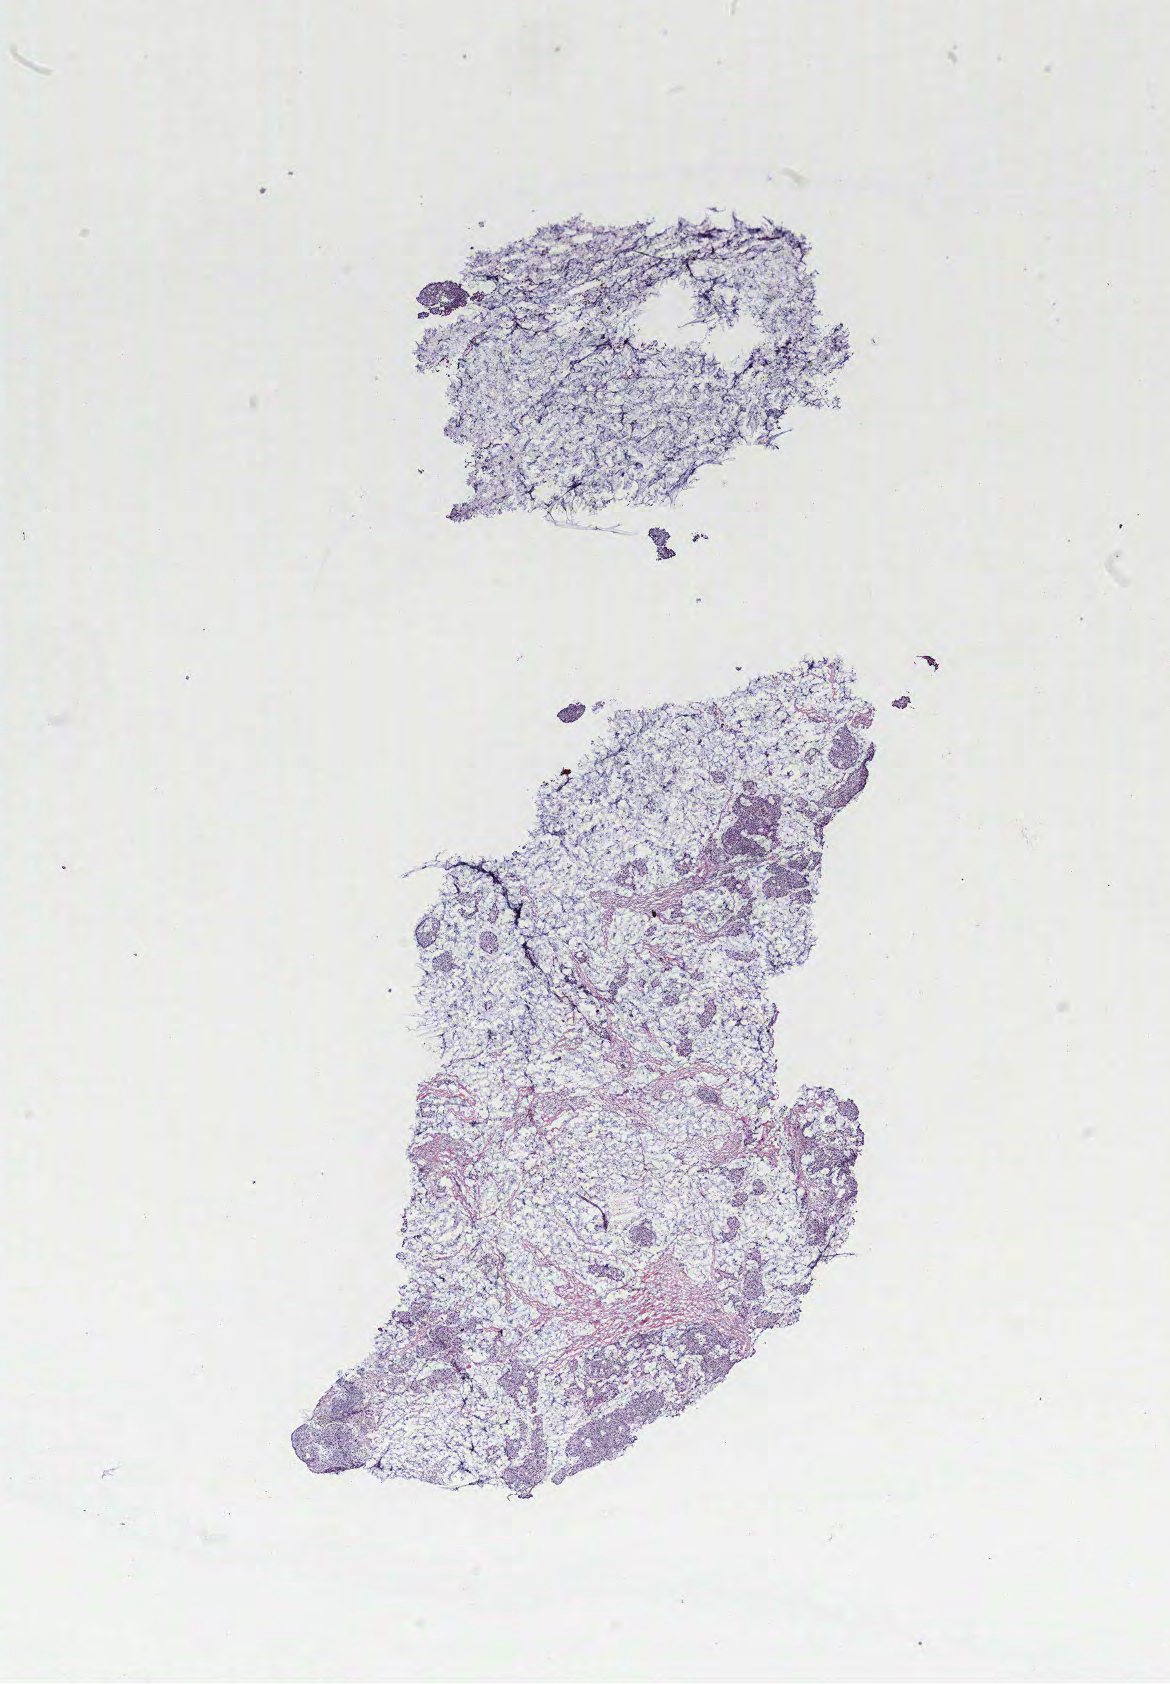
Digitized H&E-stained tissue section (whole slide) — a low-resolution overview of the entire scanned area, about 9.4 x 13.5 mm (slide scanned at 40x). Breast, tumour tissue. 82-year-old female patient.
Histologic diagnosis: Infiltrating duct carcinoma, NOS. AJCC pathologic stage: IIA.